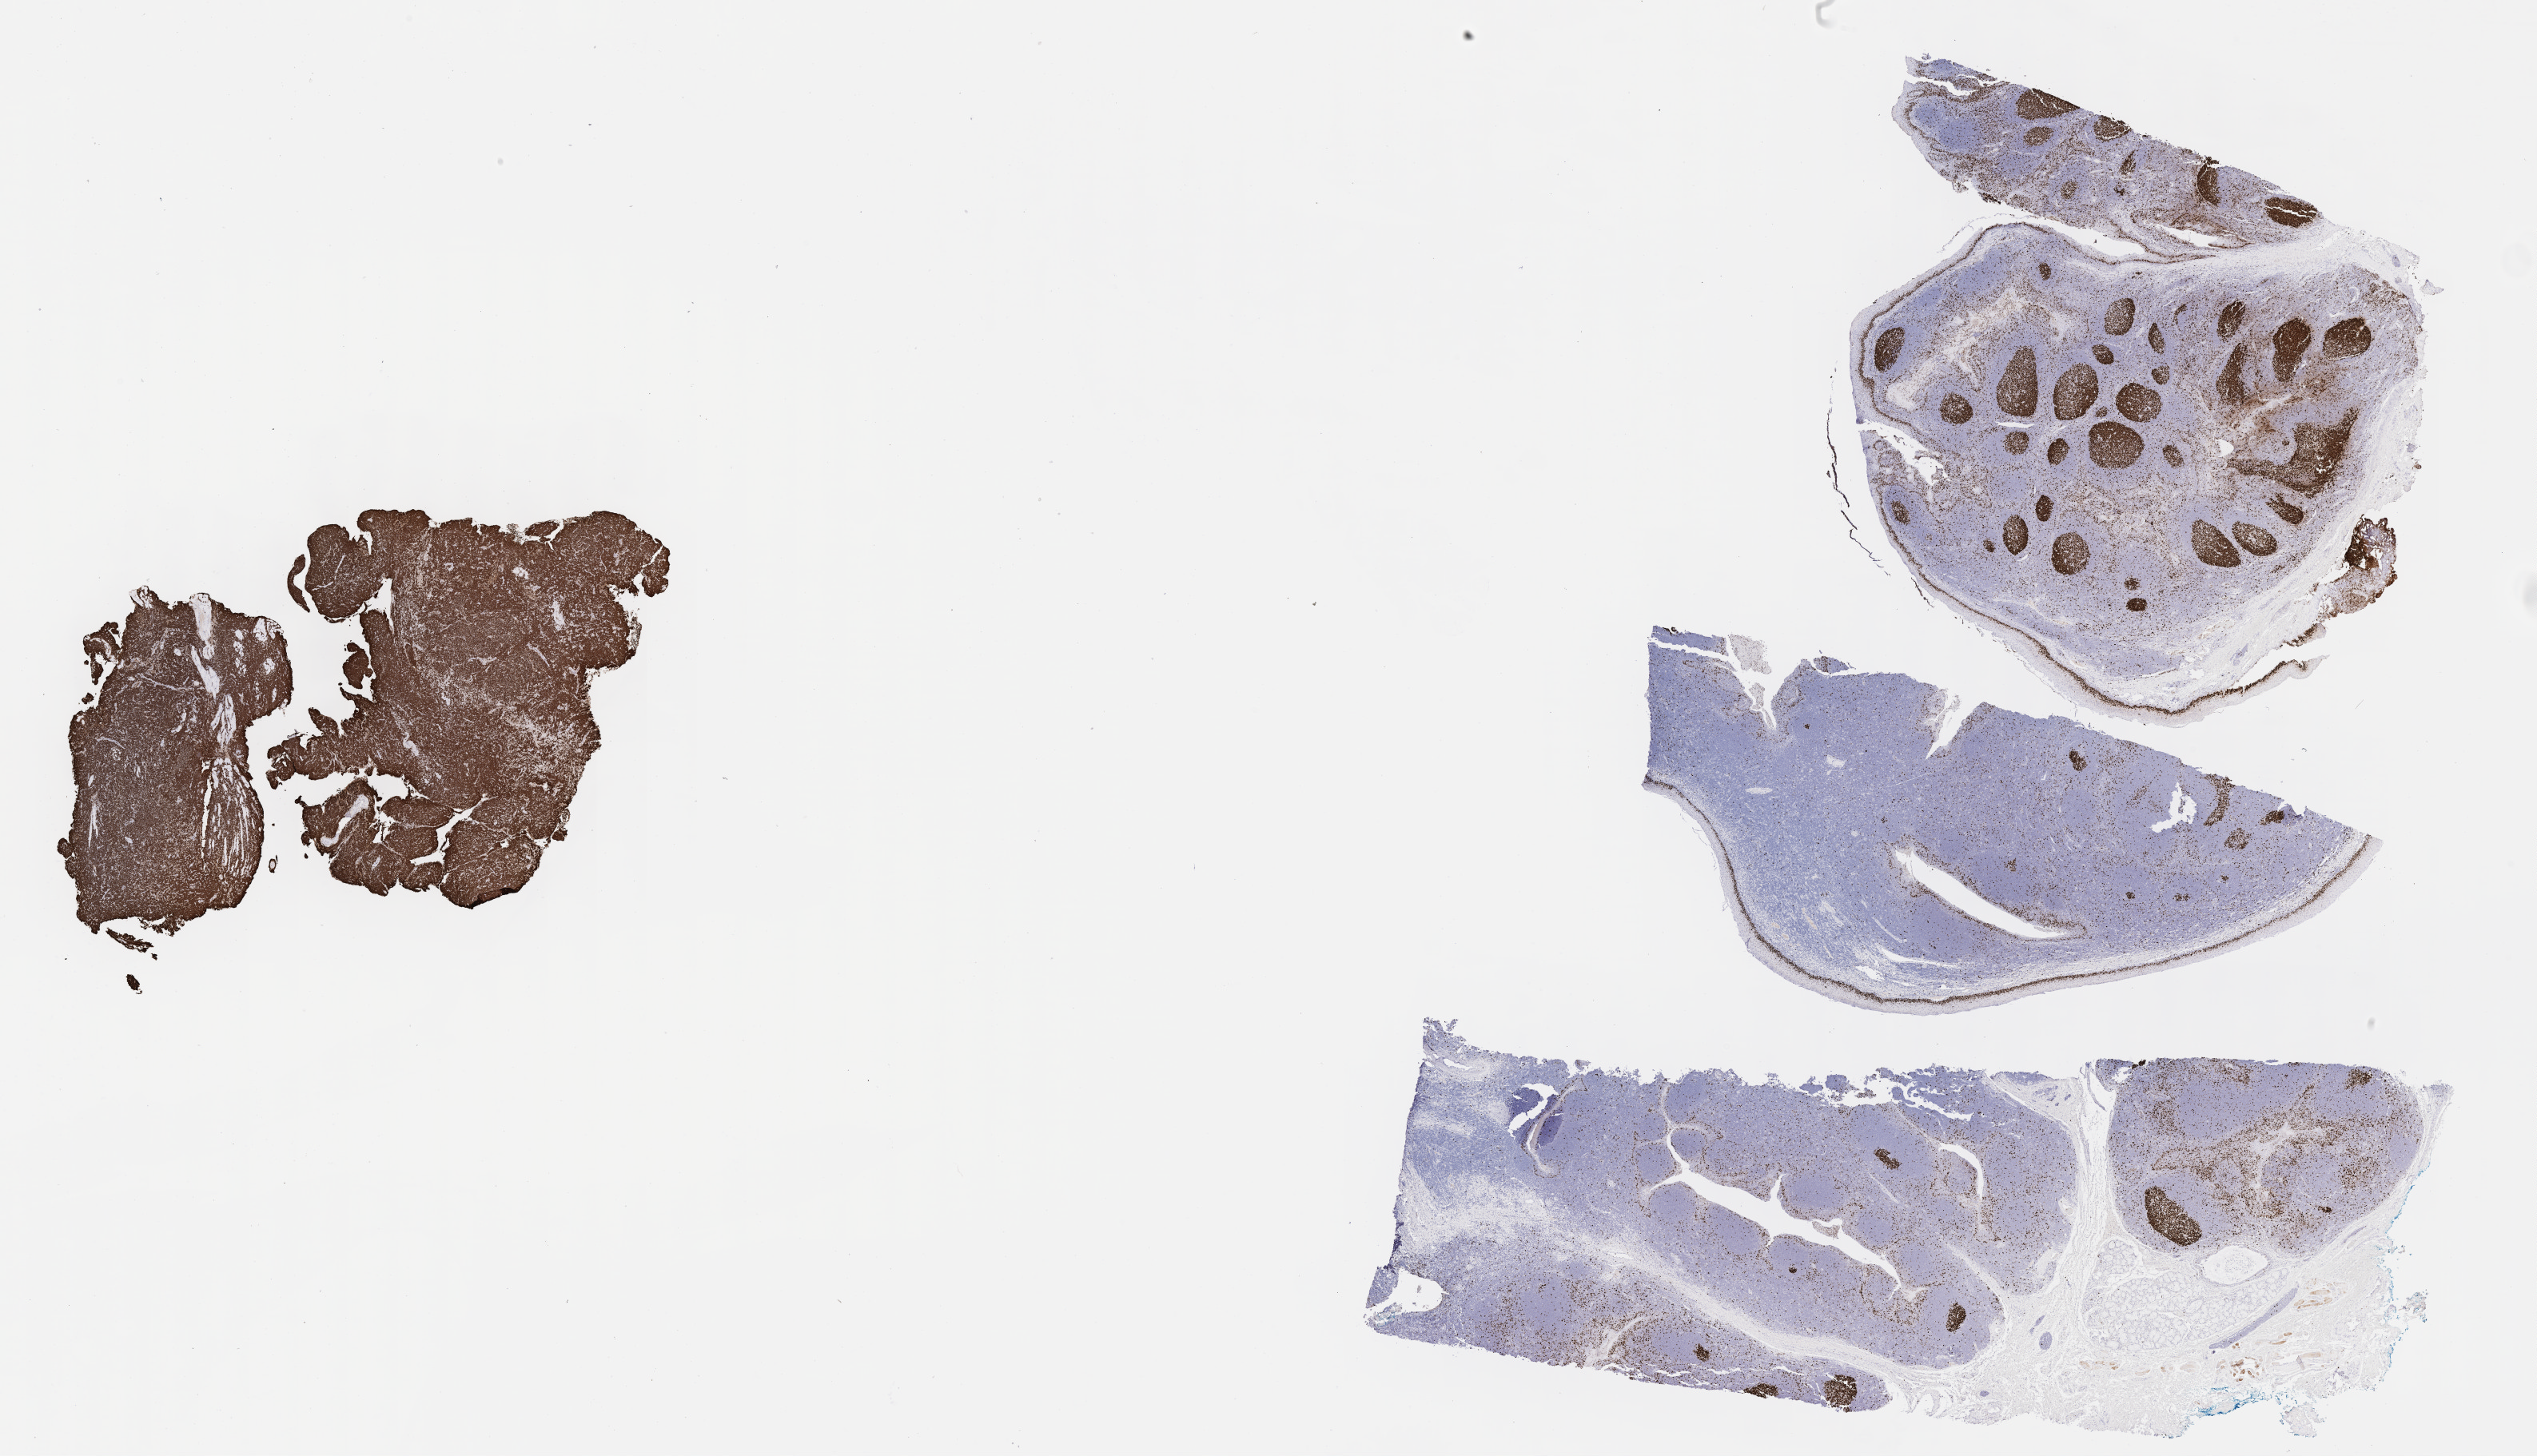
Immunohistochemistry (IHC) whole-slide image stained for Ki-67 — shown as a low-resolution overview of the whole scanned area (about 25.7 x 14.7 mm). Specimen: tumor tissue. Site: cranium. Male patient; age at initial diagnosis 8 years.
* diagnosis: Burkitt lymphoma, NOS